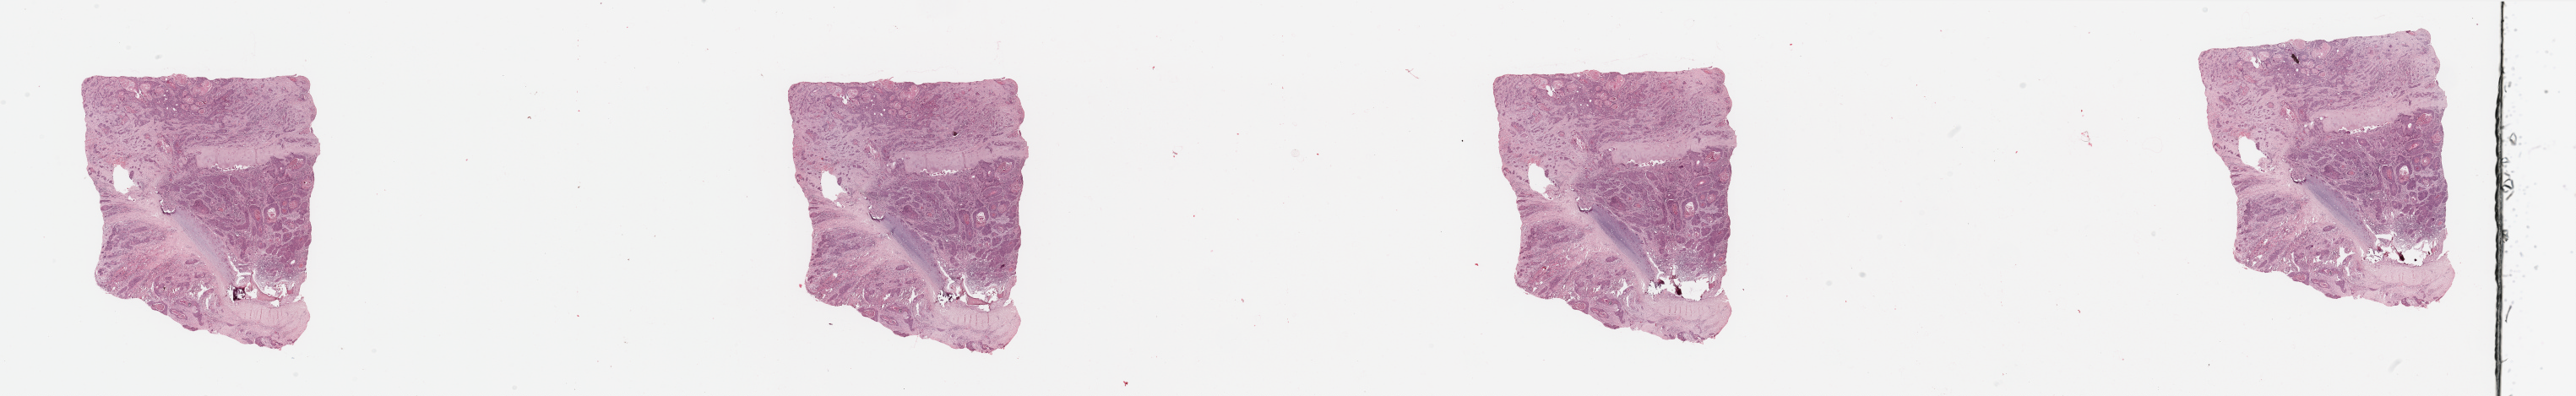
Whole-slide histology image, H&E-stained, shown as a low-resolution overview of the whole scanned area (about 48.2 x 7.4 mm, from a 20x scan). Head and neck, tissue type not recorded. Male, 81 y/o.
Patient diagnosis: Squamous cell carcinoma, NOS (larynx, NOS).